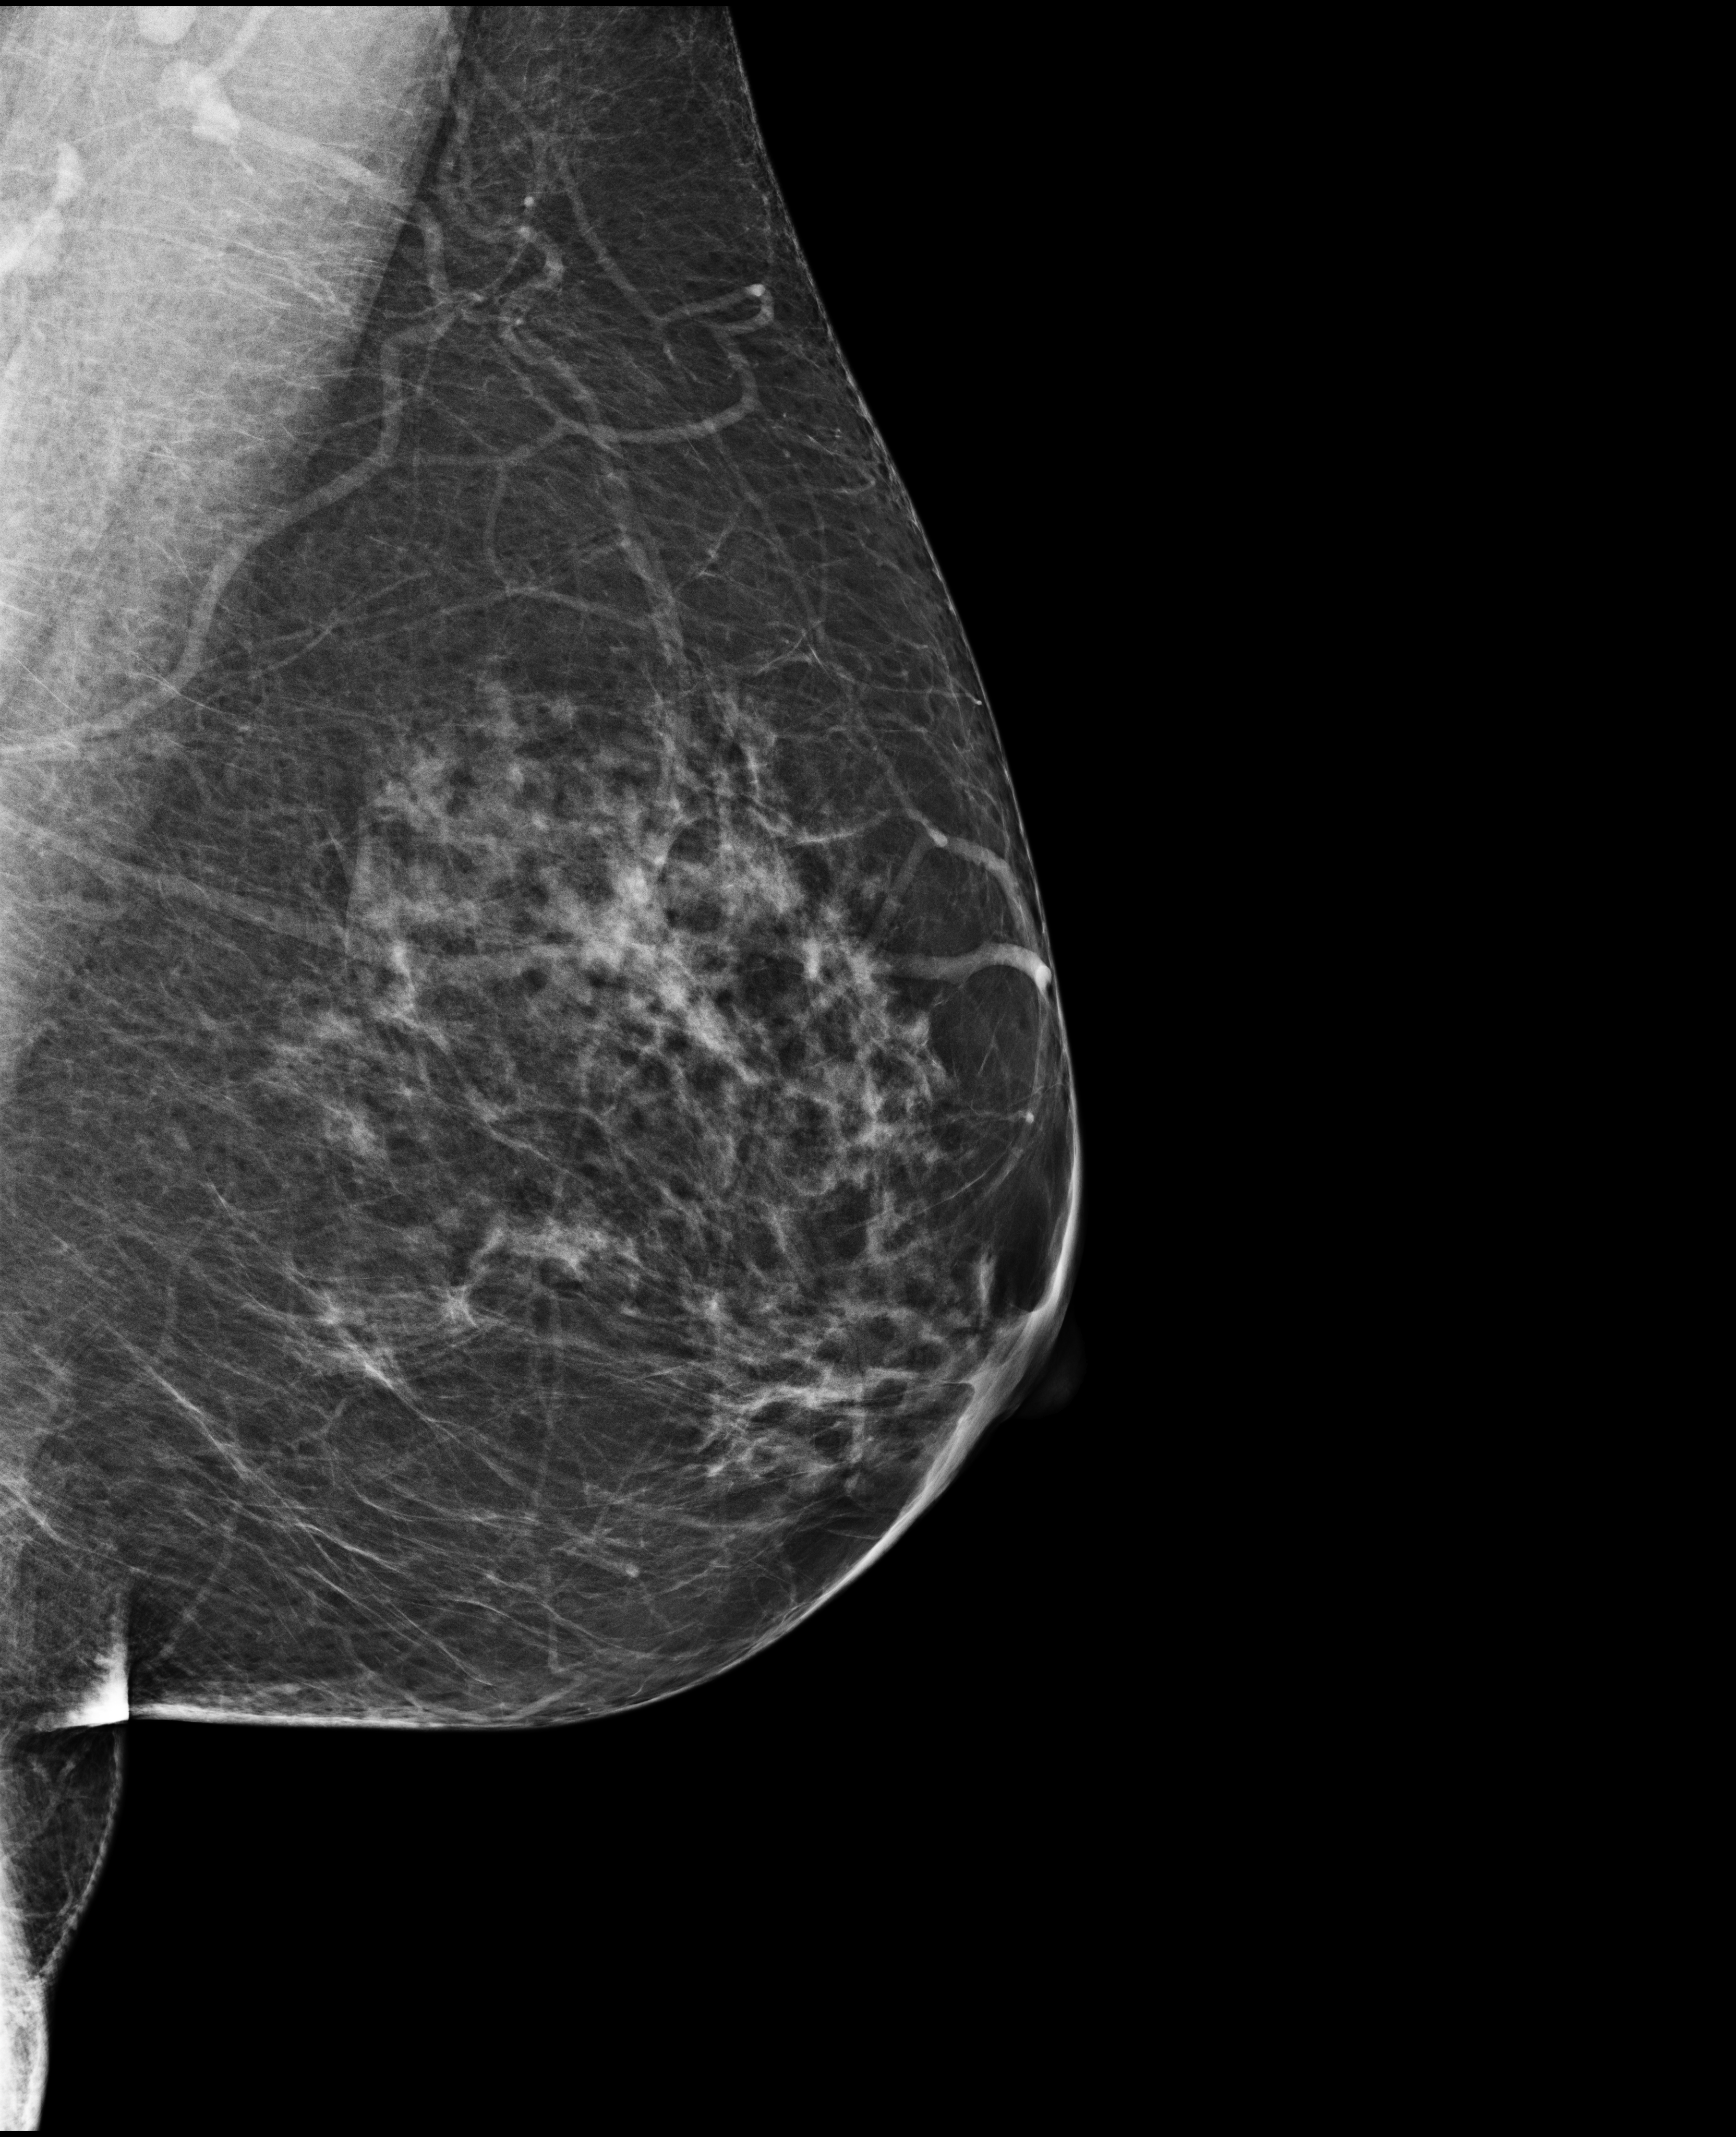
Digital mammogram (FFDM), left breast, mediolateral oblique (MLO) view, annual screening mammography examination. Patient: female, 59 years.
BI-RADS breast density category at the screening exam (both breasts, scale 1–4): 3. Final BI-RADS category for the screening round (tomosynthesis exam, both breasts): category 1. Recall: no recall after this screen.